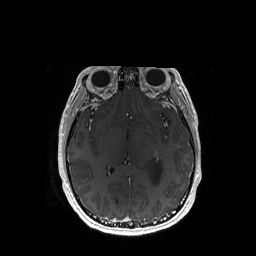
Brain MRI from a brain-tumour surgery series, one axial slice. T1-weighted post-contrast. 256 × 256 image matrix. From the clinical record (not read from this slice): histopathology: Astrocytoma; WHO grade: 3; IDH mutation: yes.
Annotated regions visible in this slice (manually delineated by an expert):
- tumour: bounding box (x1, y1, x2, y2) in pixels: (150, 158, 163, 185)